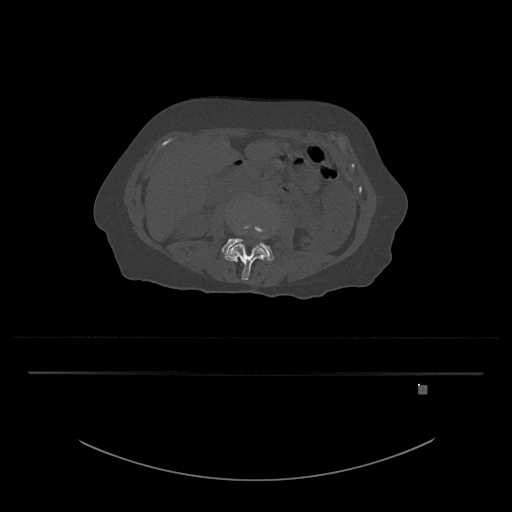
CT including the spine, one axial slice. Position 401 of 797 along the scan axis. Bone window (W 1800 / L 400 HU). 512 × 512 image matrix. Patient: female, 57 years. From the clinical record (not read from this slice): primary cancer: cervical.
Annotated regions visible in this slice (semi-automatic segmentation, software-assisted and operator-edited):
- L3 vertebra: bounding box [x1, y1, x2, y2] px = [224, 224, 267, 280]
- L4 vertebra: [221, 238, 274, 261]